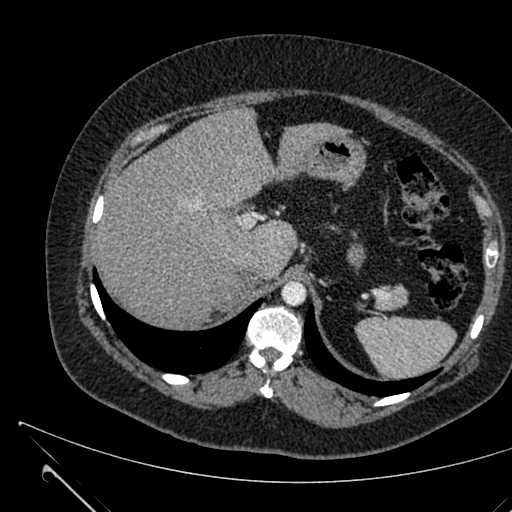
Contrast-enhanced abdominal CT, one axial slice. Position 484 of 731 along the scan axis. 120 kVp. Soft-tissue window (W 400 / L 40 HU). 1 mm slice thickness. 512 × 512 image matrix, field of view 376 × 376 mm. Patient: female, 36 years. Case-level facts recorded for this patient, not image findings: diagnosis: adrenocortical carcinoma; tumour side: right adrenal; tumour size at pathology: 10 cm.
Outlined on this slice (semi-automatic segmentation, software-assisted and operator-edited):
- mass: box from (x=213, y=279) to (x=244, y=310) px